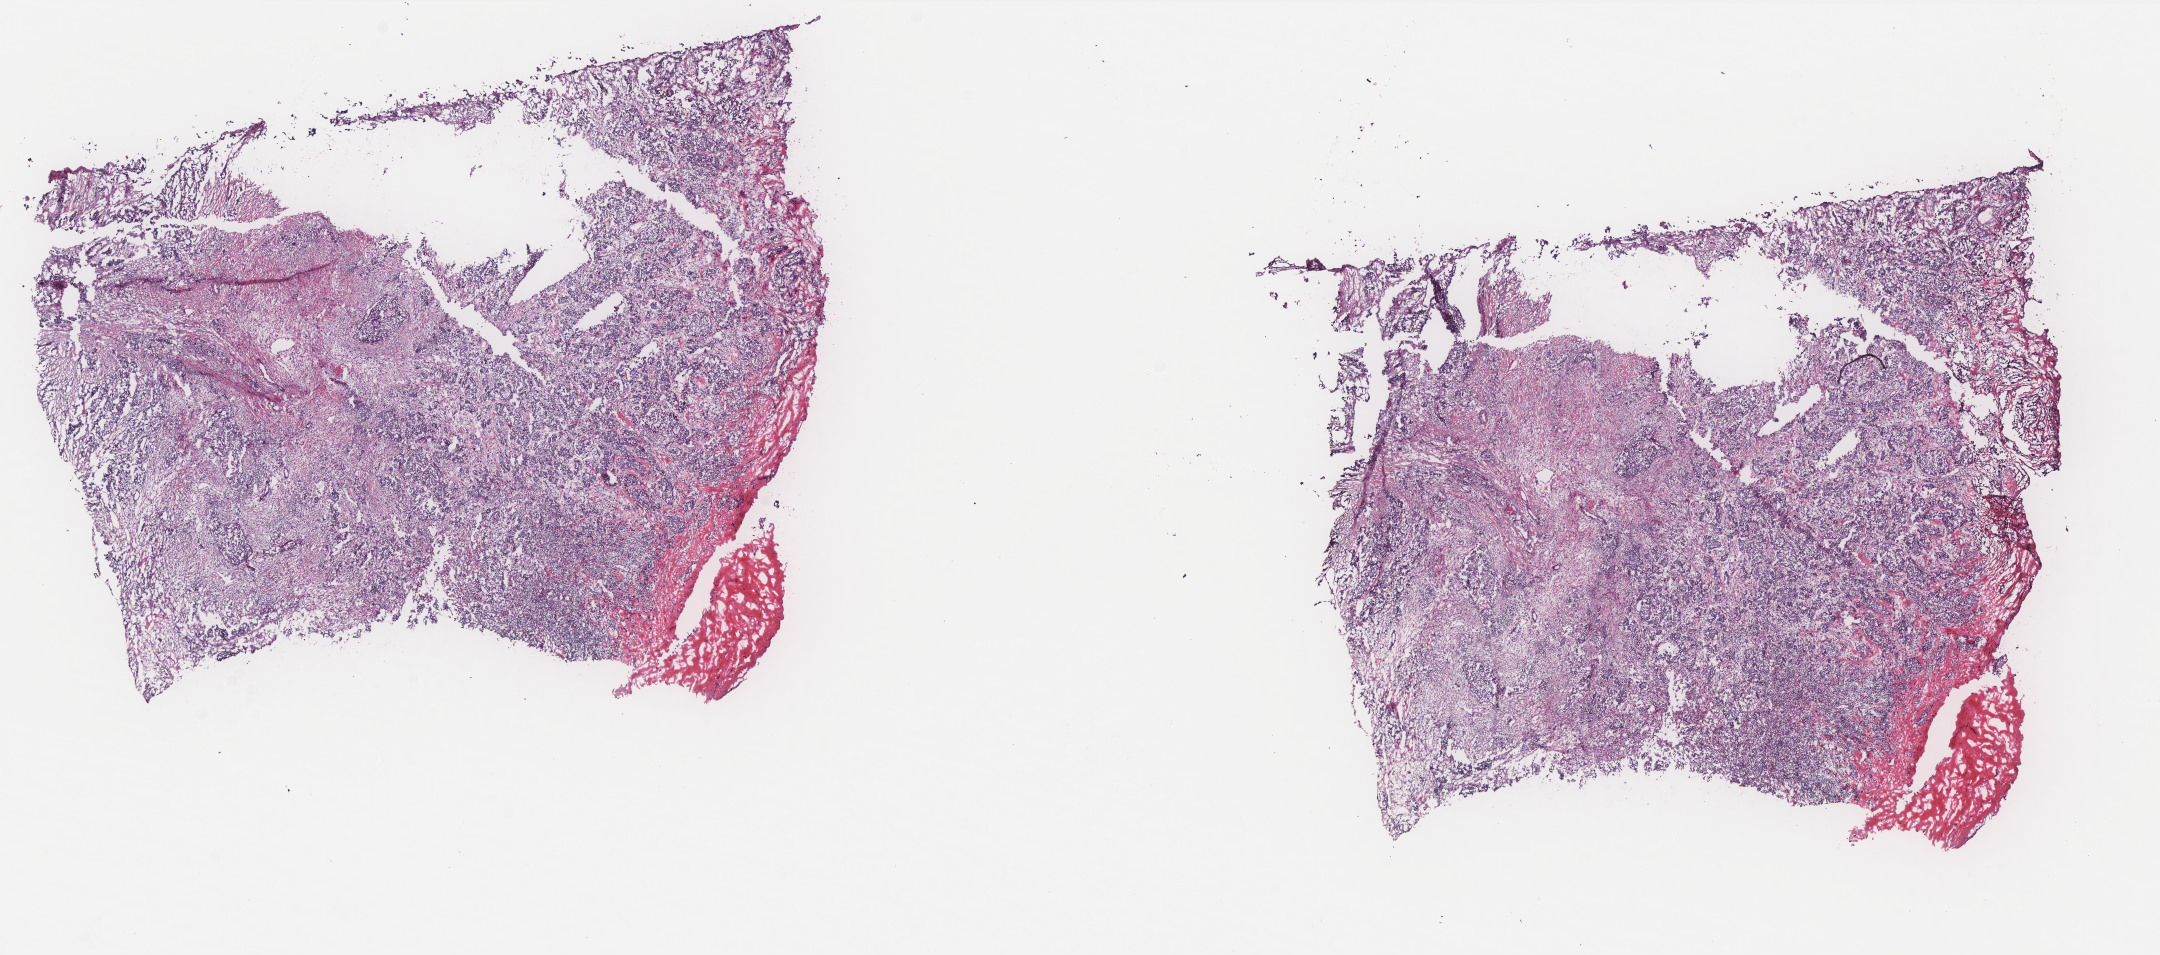
Digitized H&E-stained tissue section (whole slide) — whole scanned area (about 17.3 x 7.7 mm, acquisition: 40x scan) shown as a low-resolution overview, frozen section, primary tumour sample from the breast. Female, age 36 years at initial diagnosis. Composition of this section per pathologist review: tumour cells 80%, tumour nuclei 80%, normal cells 0%, stromal cells 20%, necrosis 0%. Infiltration values recorded for this section: lymphocyte infiltration 2%, monocyte infiltration 0%, neutrophil infiltration 0%.
TNM: T2 N2 M0. AJCC pathologic stage: IIIA (7th edition). Laterality: left. Histologic diagnosis: Infiltrating duct carcinoma, NOS.